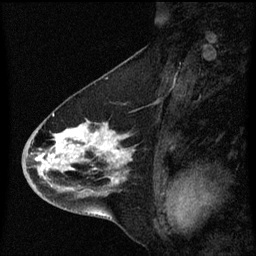
Breast MRI (dynamic contrast-enhanced), one sagittal slice. Slice 29 of 60 in the series (ordered by position). Dynamic contrast-enhanced series, image 2 of 3 at this slice position (ordered by acquisition). 1.5 T. TE 4.2 ms, TR 8.4 ms. 2 mm slice thickness. 256 × 256 image matrix, field of view 200 × 200 mm. Female patient, age 46 years. From the clinical record (not read from this slice): setting: breast cancer imaged before/during neoadjuvant chemotherapy; receptor status: HER2-positive.
Structures marked on this image (semi-automatic segmentation, software-assisted and operator-edited):
- analysis volume of interest (the breast-tissue region the enhancement analysis was run in; not a lesion): bounding box (x1, y1, x2, y2) in pixels: (22, 112, 135, 195)
- tumour enhancement mask (voxels above the 70 % enhancement threshold inside the analysis volume of interest): (43, 126, 131, 183)